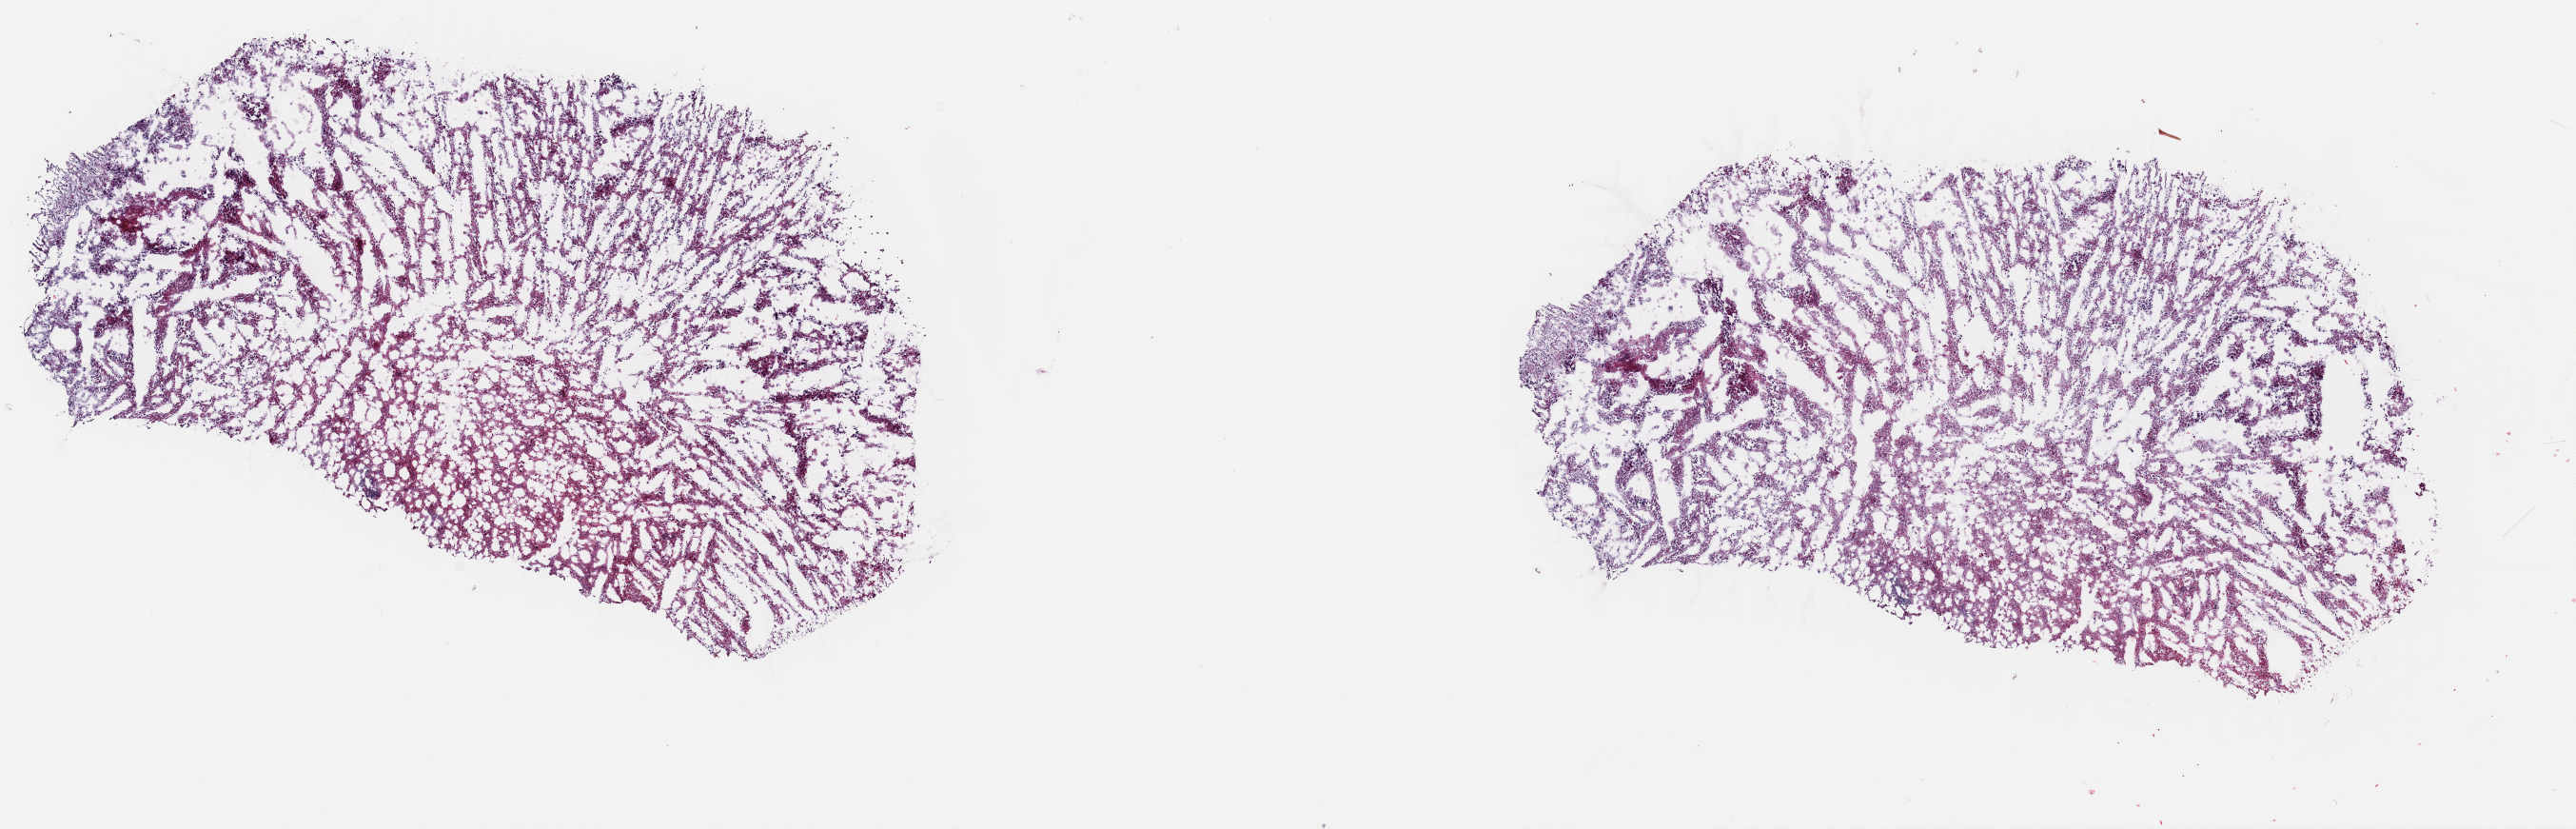
Whole-slide histology image, Hematoxylin and eosin (H&E) stained — a low-resolution overview of the entire scanned area, about 21.4 x 6.9 mm. Frozen section from the top of the tissue portion. Sample: primary tumour, brain. Patient: male, age at initial diagnosis 52 years.
Histologic diagnosis: Astrocytoma, anaplastic (cerebrum).